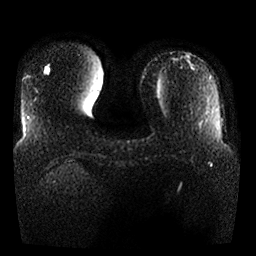
Breast MRI, one axial slice; slice 4 of 25 in the series (ordered by position); diffusion-weighted series; image 2 of 4 stored at this slice position (different b-values; order by instance number); 1.5 T; 4 mm slice thickness; 256 × 256 image matrix, field of view 360 × 360 mm. Female patient.
Annotated regions visible in this slice (outlined manually by an expert reader):
- tumour on diffusion-weighted imaging: bounding box <45,69,49,71> (left, top, right, bottom; pixels)